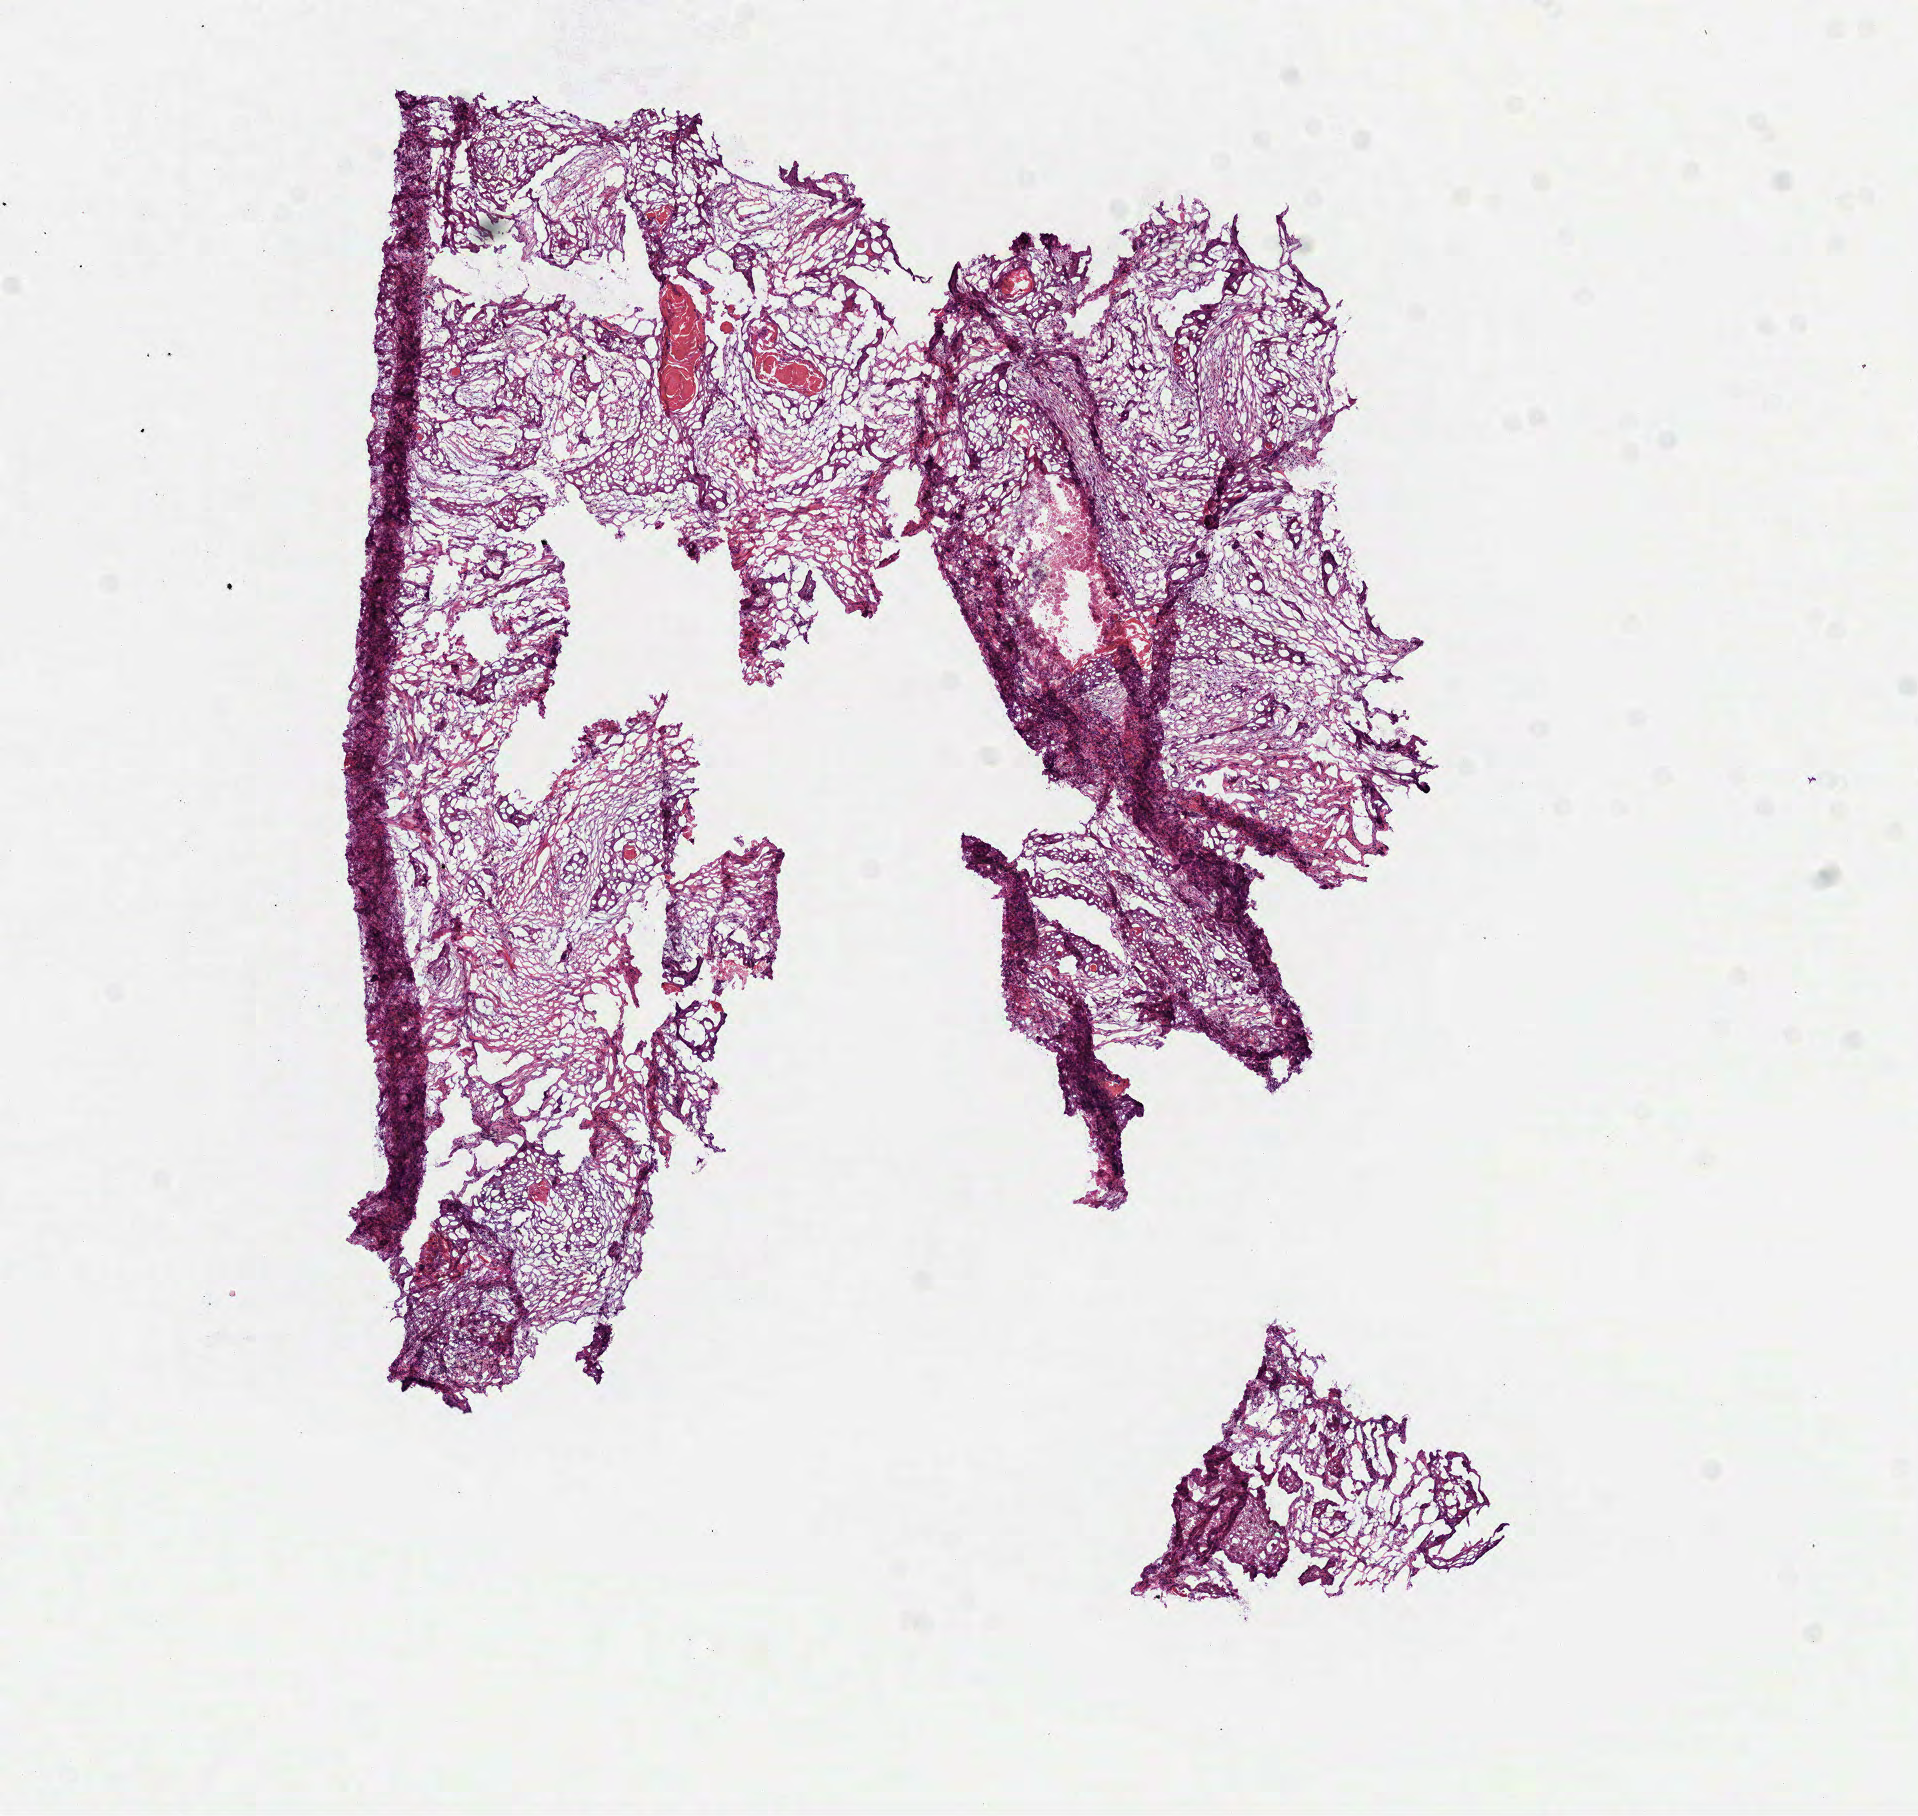
Digitized H&E-stained tissue section (whole slide), whole scanned area (about 7.7 x 7.3 mm) shown as a low-resolution overview. Frozen section. Primary tumour sample from the head and neck. Male, age 71 years at initial diagnosis. Histologic grade: G2 (moderately differentiated). Composition of this section per pathologist review: tumour cells 90%, tumour nuclei 60%, normal cells 0%, stromal cells 0%, necrosis 10%. Infiltration values recorded for this section: lymphocyte infiltration 2%, monocyte infiltration 0%, neutrophil infiltration 0%.
- AJCC pathologic stage: II (7th edition)
- pathologic diagnosis: Squamous cell carcinoma, NOS (overlapping lesion of lip, oral cavity and pharynx)